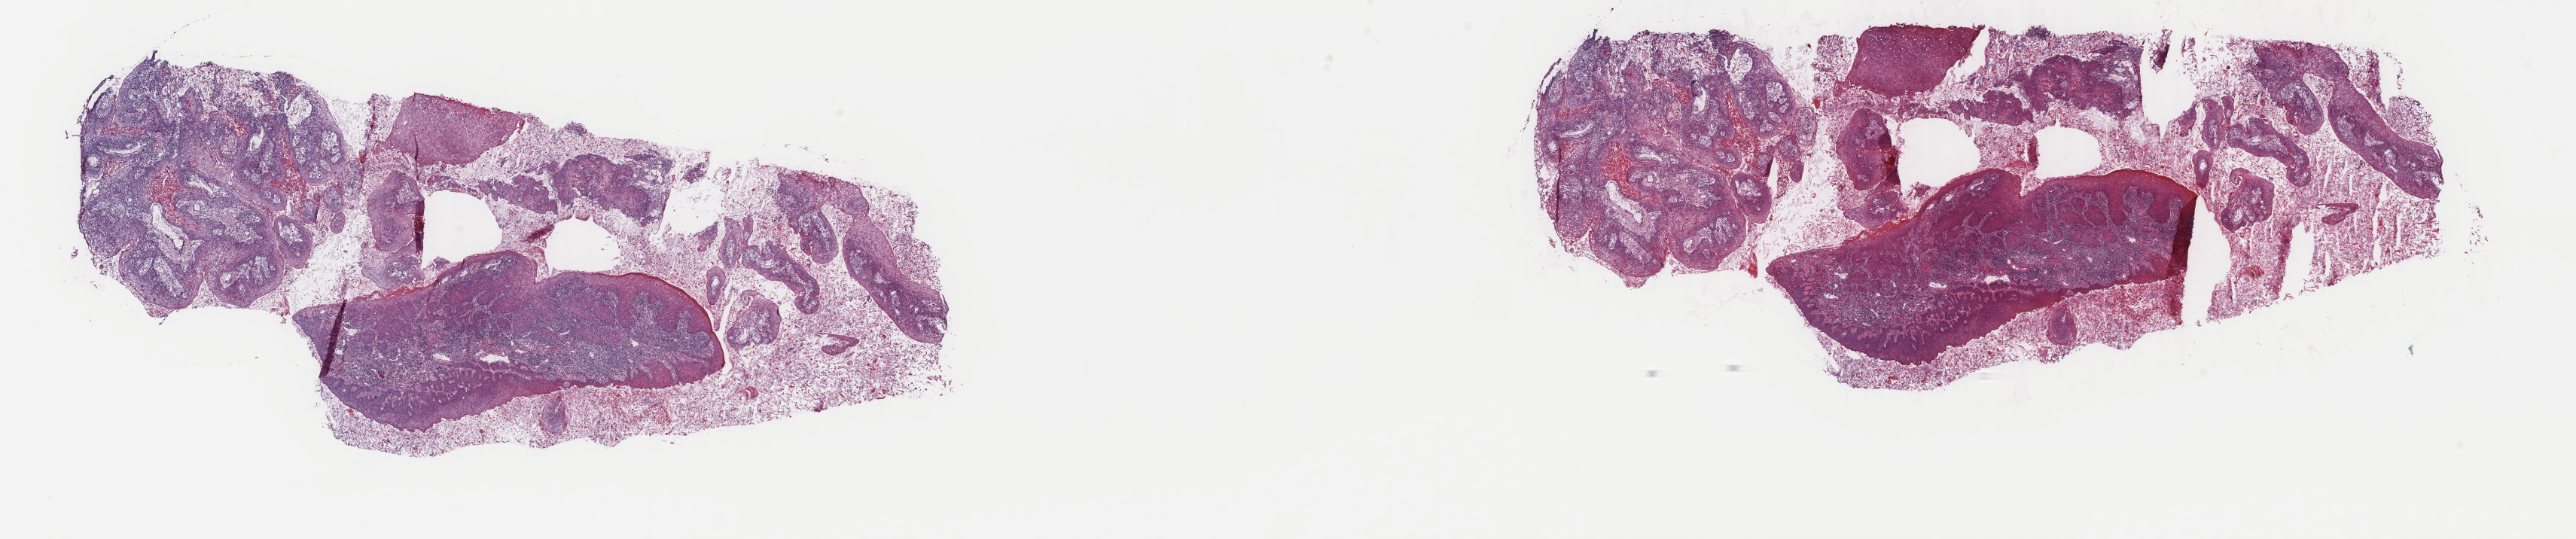
H&E whole-slide image — a low-resolution overview of the entire scanned area, about 27.2 x 5.7 mm (from a 40x scan). Frozen section. Sample: primary tumour, head and neck. Female patient; age at initial diagnosis 80 years. Histologic grade: G2 (moderately differentiated). Pathologist review of this section (percent, as recorded): tumour cells 70%, tumour nuclei 70%, normal cells 10%, stromal cells 20%, necrosis 0%. Inflammatory infiltration, as recorded: lymphocyte infiltration 5%, monocyte infiltration 0%, neutrophil infiltration 0%.
AJCC pathologic stage: IVA (7th edition). TNM: T4a N0 M0. Lymph nodes positive (case pathology): 0 of 28 examined. Laterality: left. Histologic diagnosis: Squamous cell carcinoma, NOS (floor of mouth, NOS).